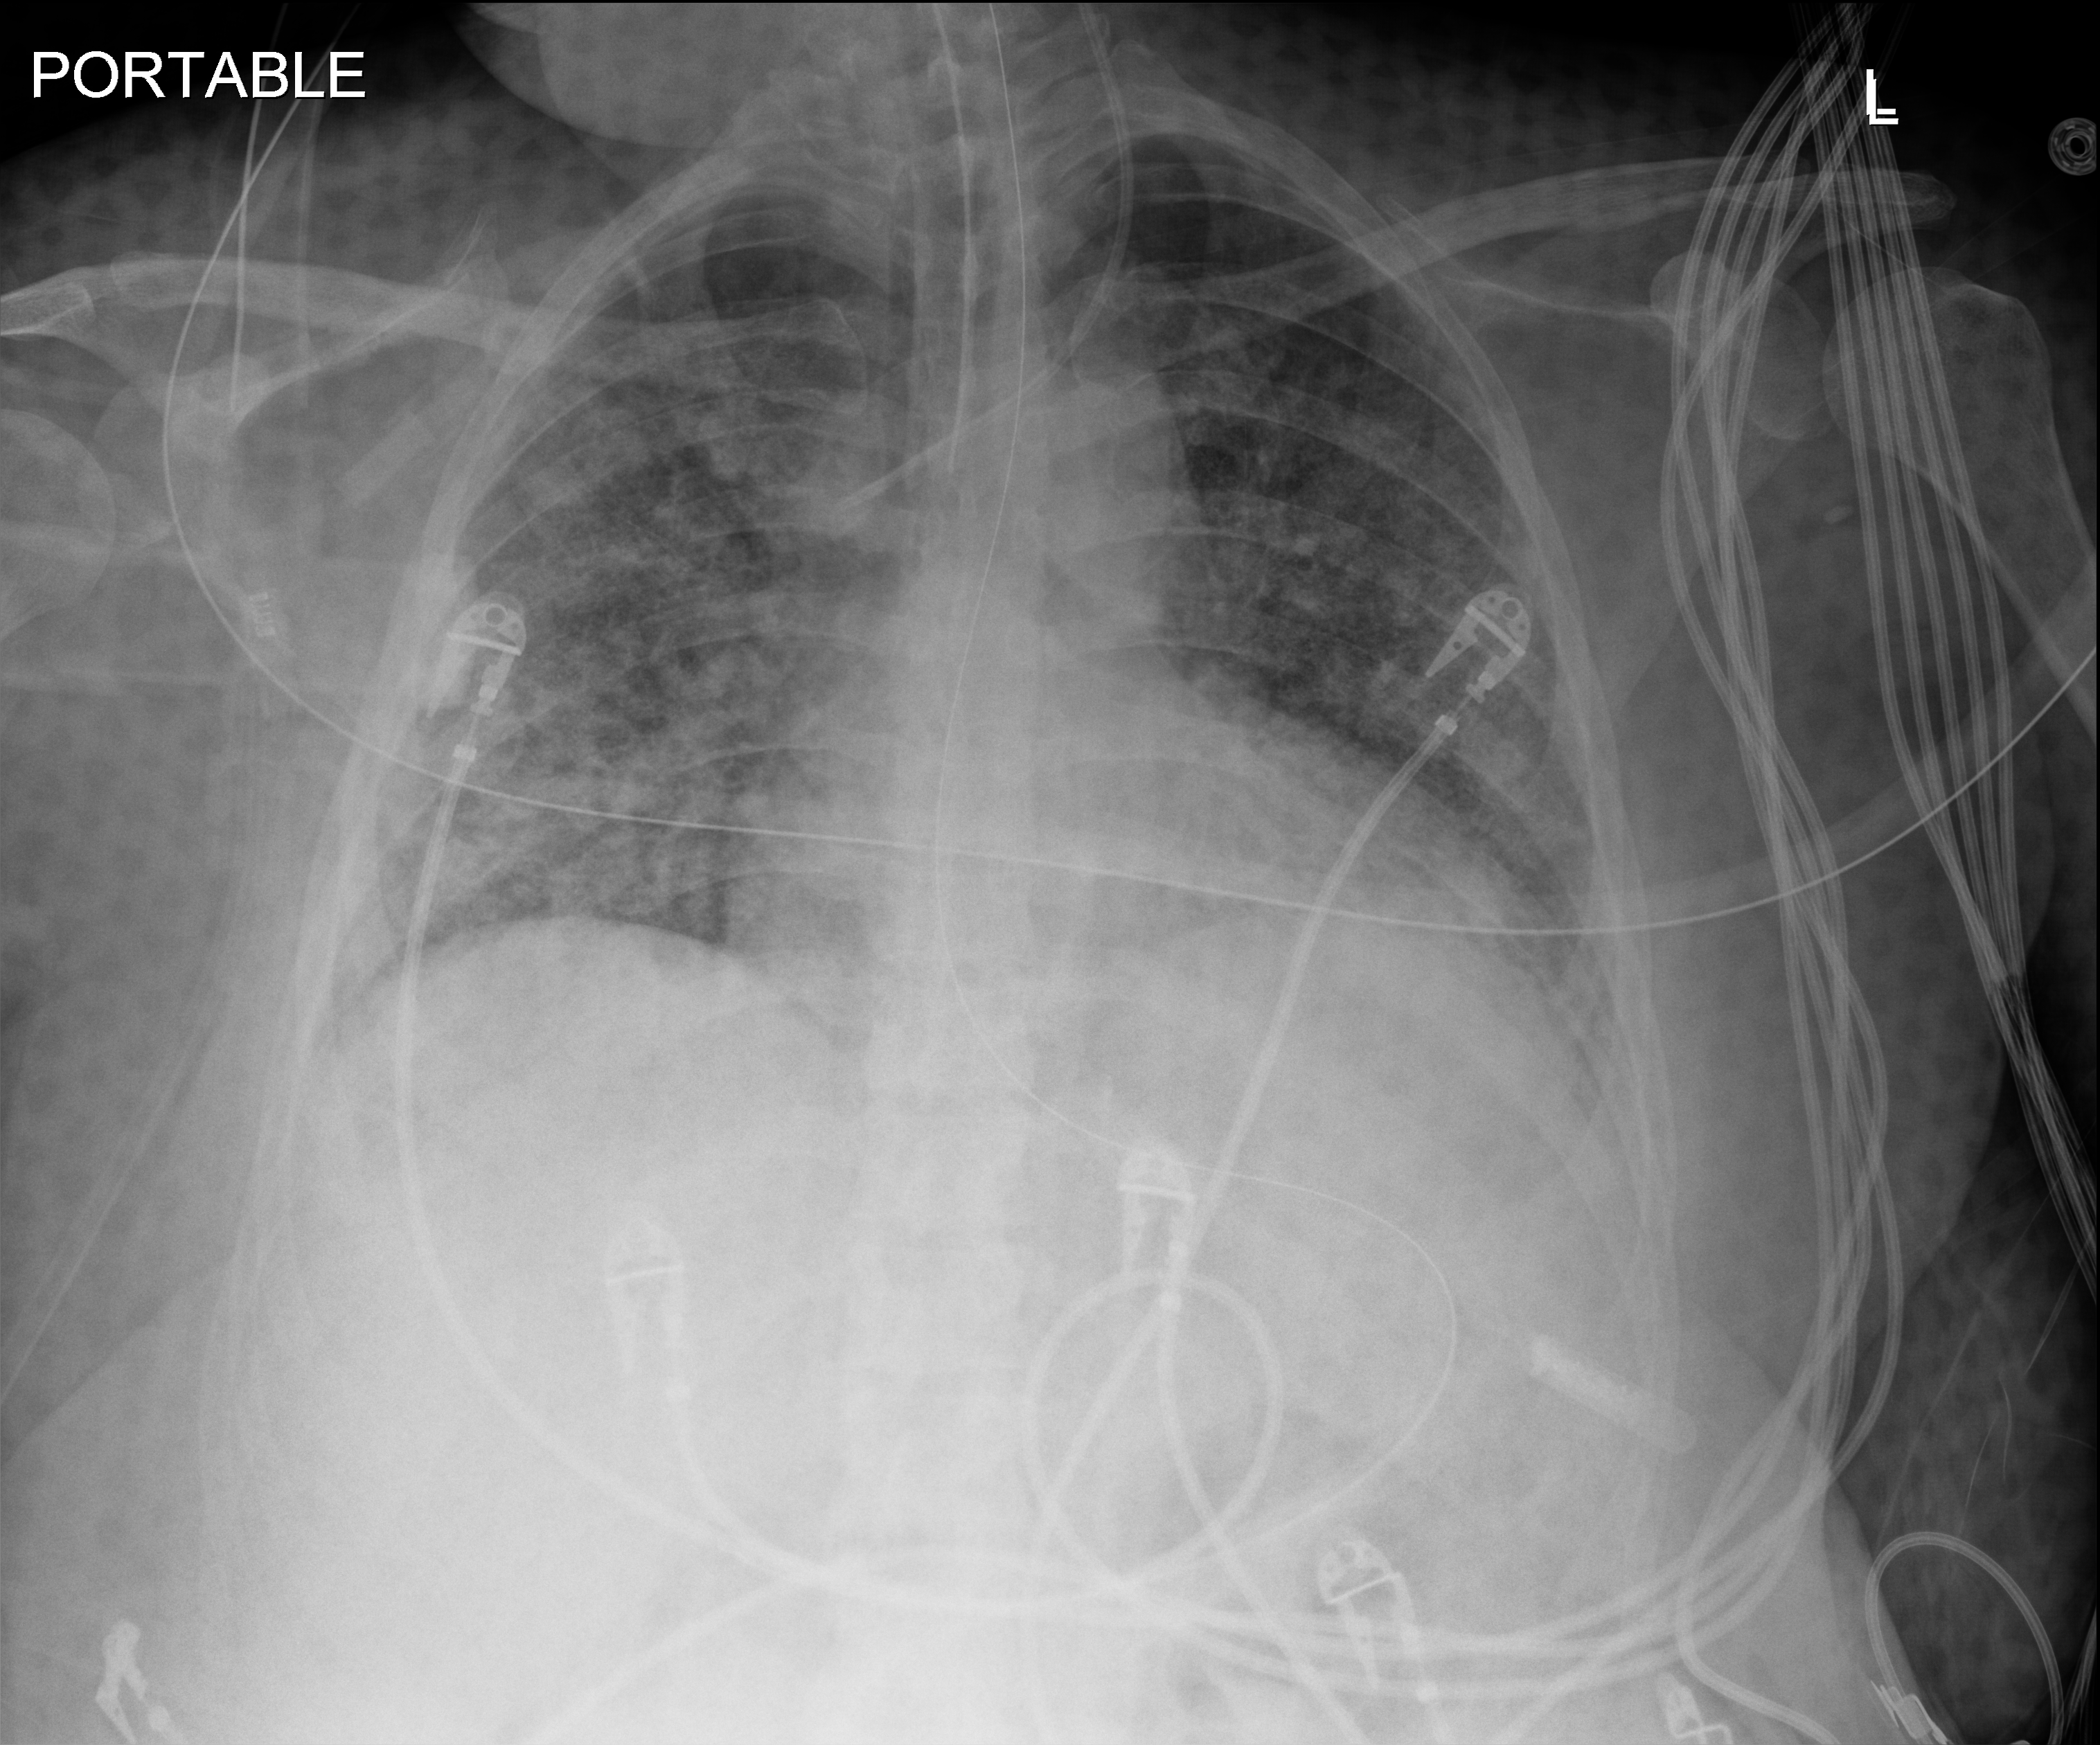
Chest X-ray. Patient hospitalised with COVID-19; female, aged 18–59 years.
Hospital-stay facts (about this admission, not read from this image; timing relative to this image not recorded): length of hospital stay: 33 days.